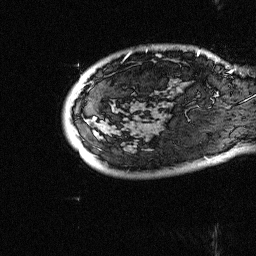
Breast MRI (dynamic contrast-enhanced), one sagittal slice; dynamic contrast-enhanced study with each time point stored as its own series, time point 2 of 3 at this slice position (early post-contrast, ordered by acquisition time); 1.5 T; TE 4.5 ms, TR 11 ms; 2.5 mm slice thickness; 256 × 256 image matrix, field of view 200 × 200 mm. Patient: female, 38 years. From the clinical record (not read from this slice): setting: breast cancer imaged before/during neoadjuvant chemotherapy; receptor status: HR-positive, HER2-negative.
Annotated regions visible in this slice (semi-automatically segmented with operator editing):
- analysis volume of interest (the breast-tissue region the enhancement analysis was run in; not a lesion): bounding box (x1, y1, x2, y2) in pixels: (88, 20, 252, 126)
- tumour enhancement mask (voxels above the 90 % enhancement threshold inside the analysis volume of interest): (156, 54, 161, 57)